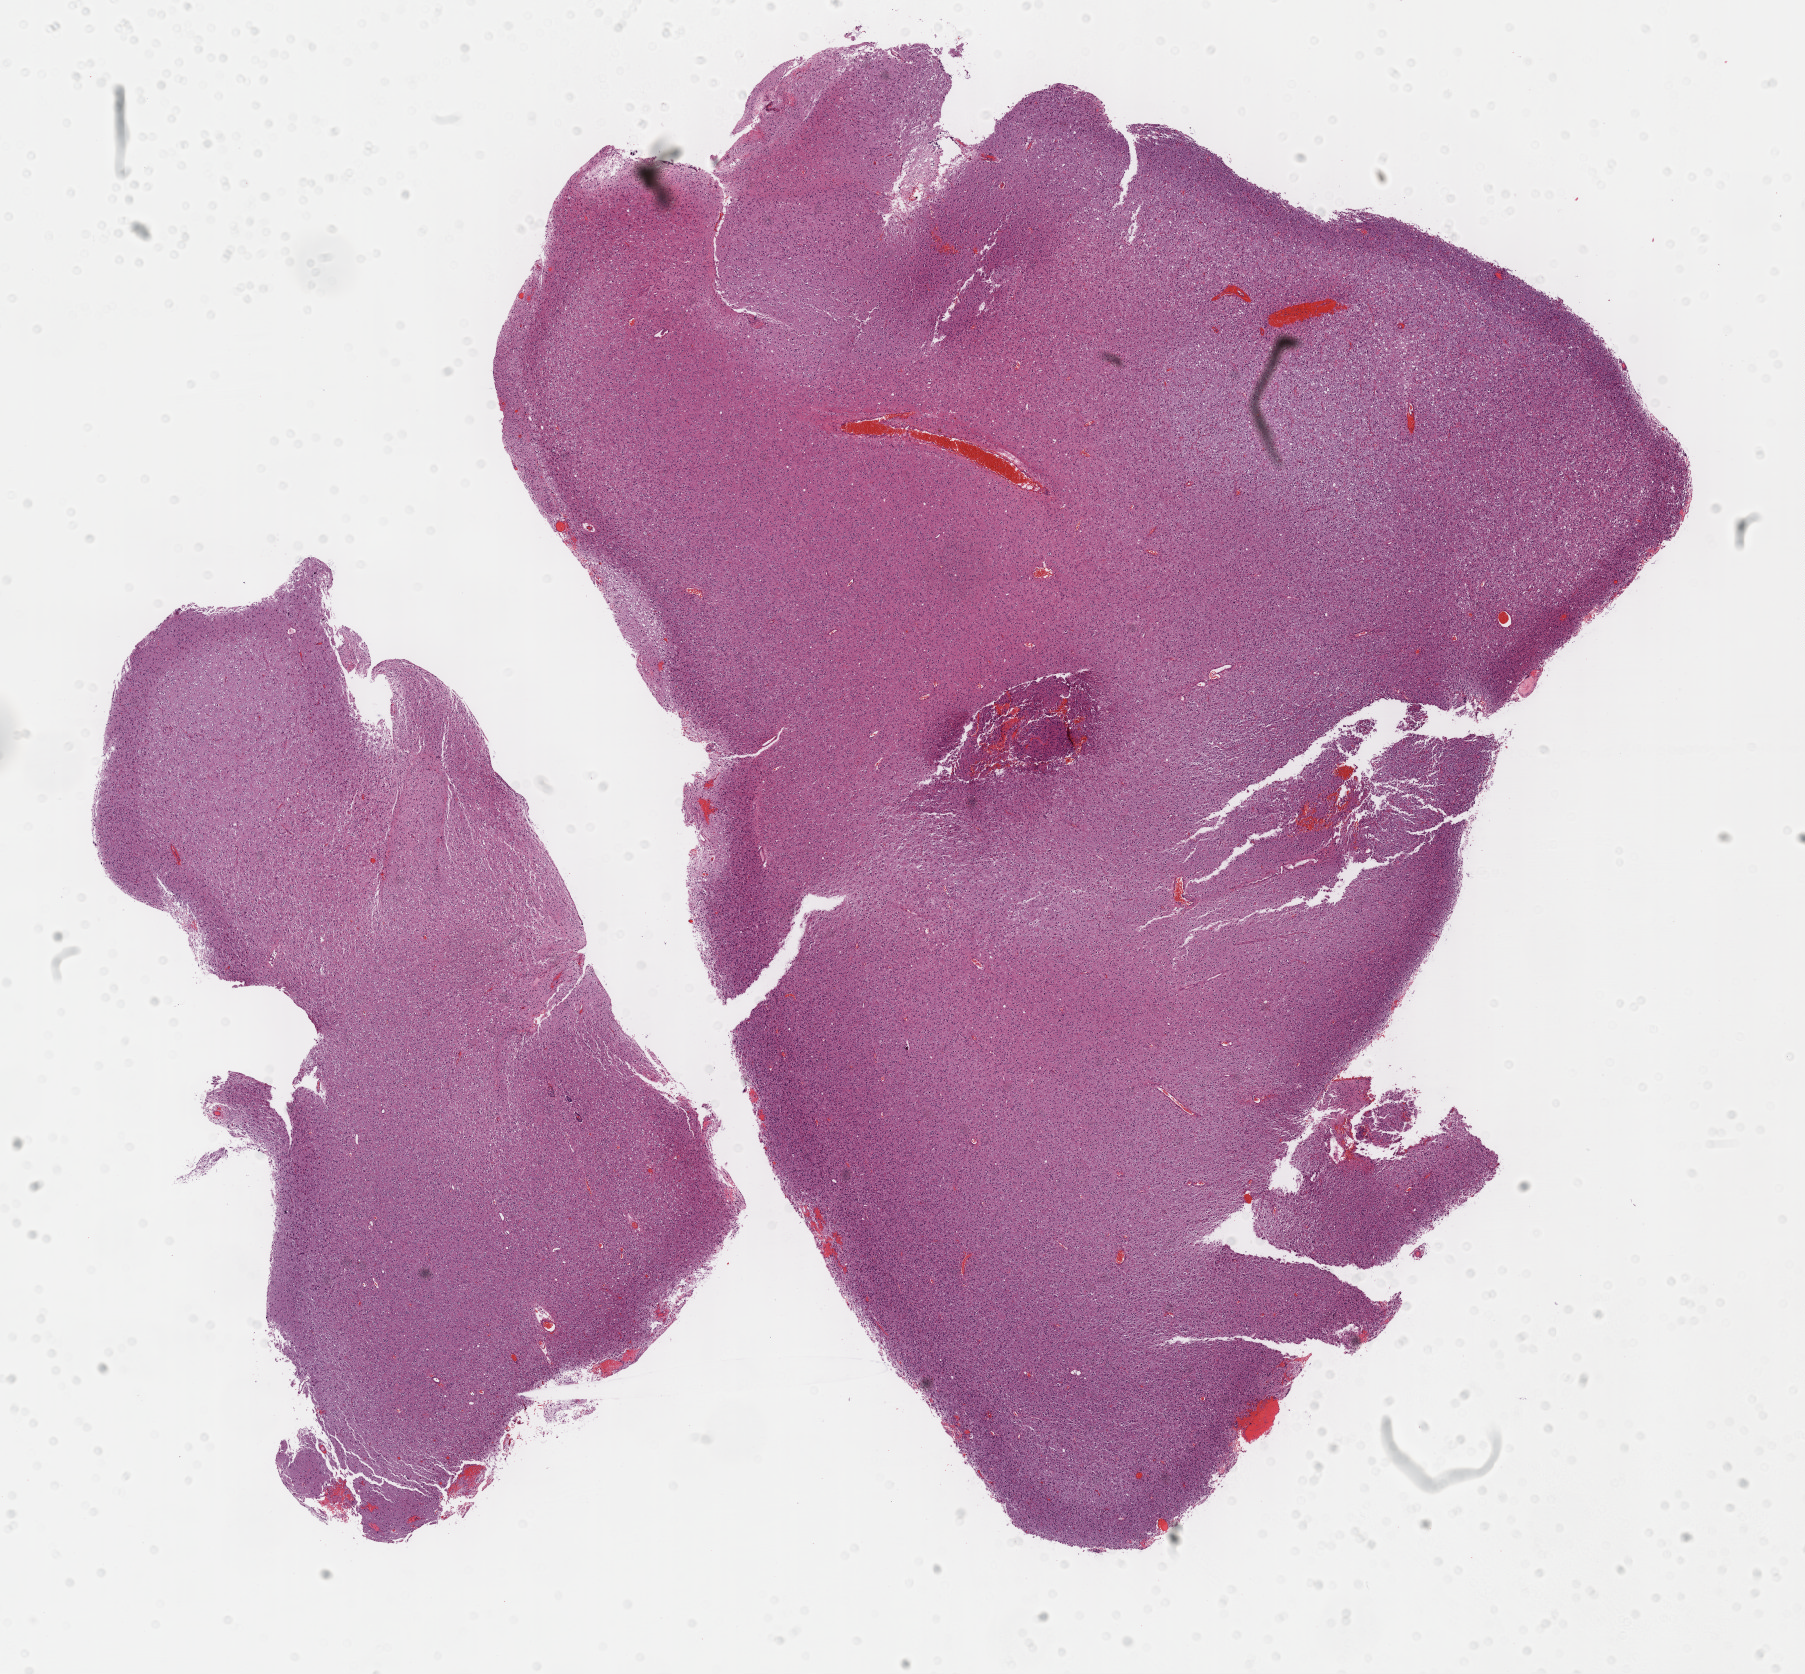
Hematoxylin and eosin (H&E) stained whole-slide image — a low-resolution overview of the entire scanned area, about 14.6 x 13.5 mm. Formalin-fixed paraffin-embedded (FFPE) diagnostic section. Brain, primary tumour sample. Patient: male, age at initial diagnosis 37 years. Histologic grade: G3 (poorly differentiated).
* histologic diagnosis: Oligodendroglioma, anaplastic